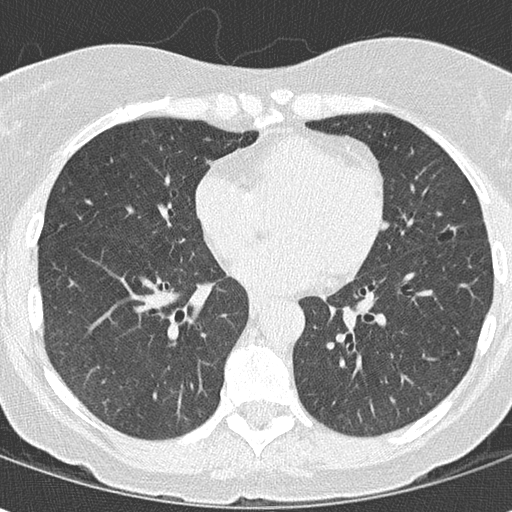
Low-dose screening chest CT, axial slice, second annual screen, lung window (W 1500 / L -600 HU), slice 80 of 163 in the series. Female, age 63 years at enrolment. Current smoker at enrolment.
- Lesion marked by an expert reader, bounding box (x1, y1, x2, y2) in pixels: (422, 209, 477, 255).
- The screening reader recorded 4 non-calcified nodules or masses ≥4 mm on this exam; which of them this box marks is not recorded.
- Official screen result: positive, other.
- Later outcome: lung cancer diagnosed 504 days after this screen (after the third annual screen) — bronchiolo-alveolar adenocarcinoma, NOS, lingula, stage IA (AJCC 6th edition), 14 mm at pathology.